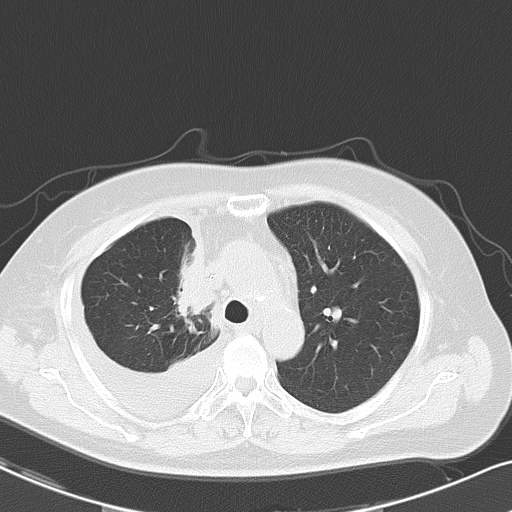
Chest CT, one axial slice; position 36 of 48 along the scan axis; reconstruction kernel B70f; 120 kVp; lung window (W 1500 / L -600 HU); 512 × 512 image matrix, field of view 328 × 328 mm. Female patient, age 69 years. Case-level facts recorded for this patient, not image findings: clinical TNM (as recorded): T2a N0 M1c.
Annotated regions visible in this slice (rectangle marked by the reading radiologist):
- lung tumour (recorded histology: adenocarcinoma): box from (x=172, y=219) to (x=213, y=324) px